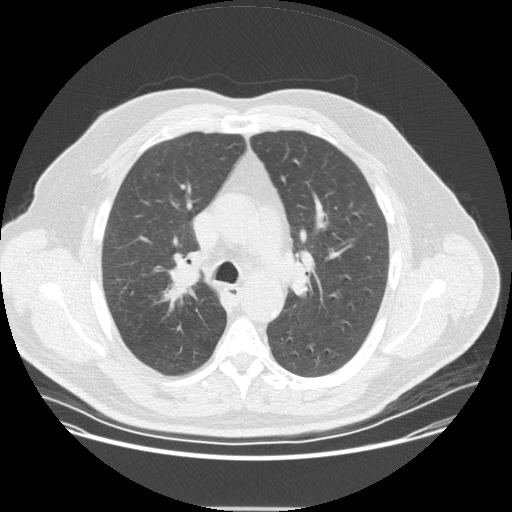
Chest CT (low-dose screening protocol), one axial image; second screening round (one year after baseline); lung window (W 1500 / L -600 HU); 2.5 mm slice thickness; standard (soft-tissue) reconstruction kernel (STANDARD); slice 119 of 351 in the series; 512 × 512 image matrix, field of view 419 × 419 mm. Male, age 57 years at enrolment. Current smoker at enrolment.
- Expert reader's lesion annotation, bounding box (x1, y1, x2, y2) in pixels: (148, 251, 211, 311).
- Reader record for this screening exam (exam-level; its link to the box is not recorded): non-calcified nodule or mass ≥4 mm, right upper lobe, 20 × 16 mm, spiculated (stellate) margins, soft tissue attenuation, pre-existing on the prior screen: no.
- Official screen result: positive, other.
- Later outcome: lung cancer diagnosed 35 days after this screen — non-small cell carcinoma, right upper lobe, poorly differentiated (G3), stage IIA (AJCC 6th edition), 25 mm at pathology.